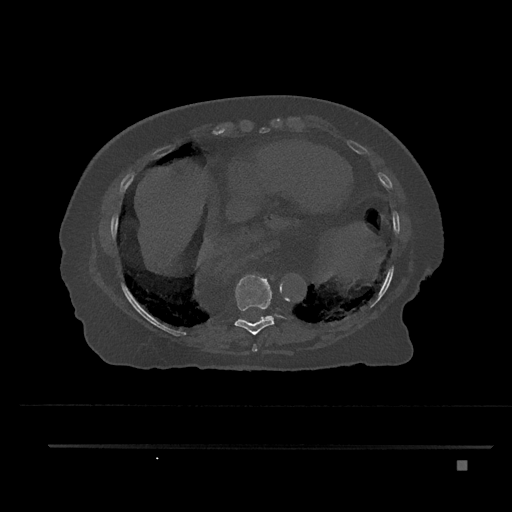
CT including the spine, one axial slice; slice 394 of 797 in the series (ordered by position); bone window (W 1800 / L 400 HU); 512 × 512 image matrix. Female patient, age 76 years. Case-level facts recorded for this patient, not image findings: primary cancer: lung; vertebrae with lytic lesions (as recorded): T11, L3.
Outlined on this slice (semi-automatically segmented with operator editing):
- T8 vertebra: bounding box [x1, y1, x2, y2] px = [252, 344, 257, 352]
- T9 vertebra: [234, 275, 275, 335]